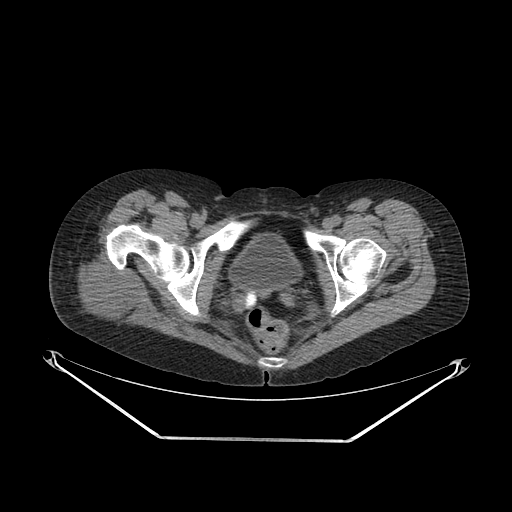
CT of an extremity soft-tissue mass (from a PET/CT study), one axial slice. Position 47 of 267 along the scan axis. 140 kVp. Soft-tissue window (W 400 / L 40 HU). 3.75 mm slice thickness. 512 × 512 image matrix, field of view 500 × 500 mm. Female patient. From the clinical record (not read from this slice): histological type: epithelioid sarcoma with vascular differentiation; site of the primary tumour: right buttock.
Structures marked on this image (expert contour drawn on MRI and transferred to this co-registered scan by the dataset authors):
- gross tumour volume (mass): bounding box (x1, y1, x2, y2) in pixels: (69, 254, 152, 332)